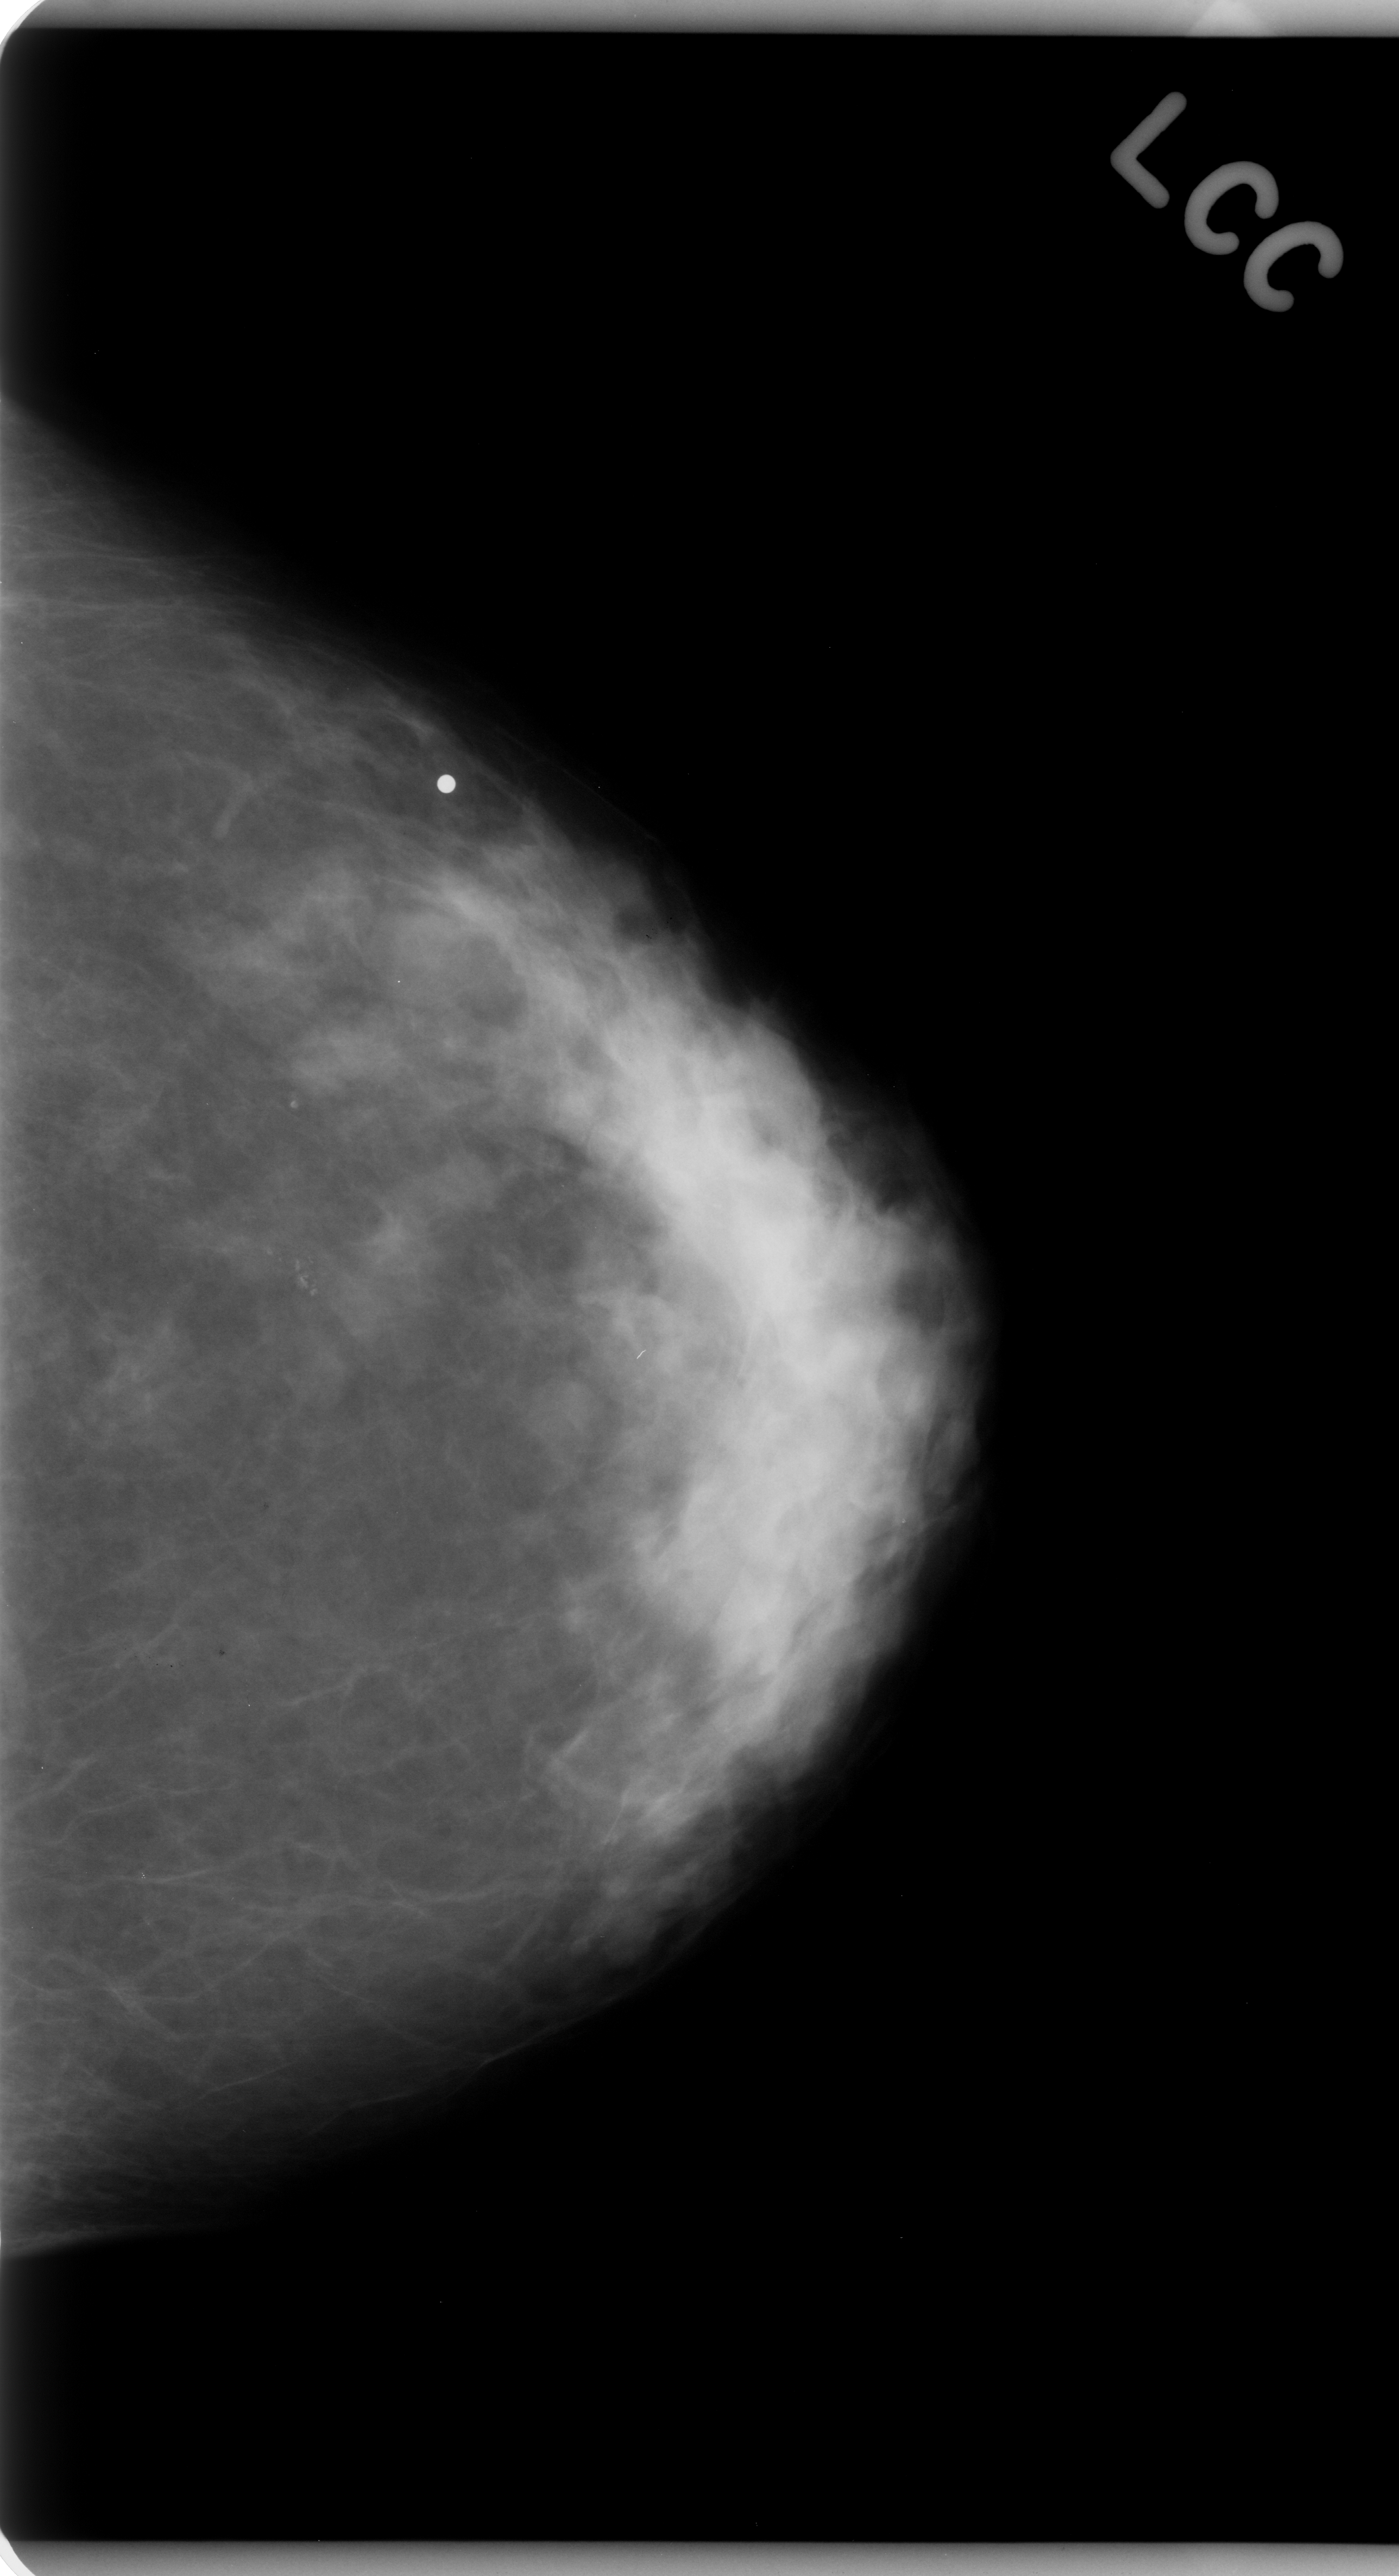
Digitized screen-film mammogram. Left breast. Craniocaudal (CC) view. Breast composition: heterogeneously dense (BI-RADS density category 3 of 4). 1399 × 2576 image matrix.
Marked abnormalities (boxes around the expert regions of interest):
- calcifications, morphology amorphous, distribution clustered; BI-RADS assessment category 4; pathology (as recorded): benign: box from (x=212, y=1159) to (x=388, y=1317) px